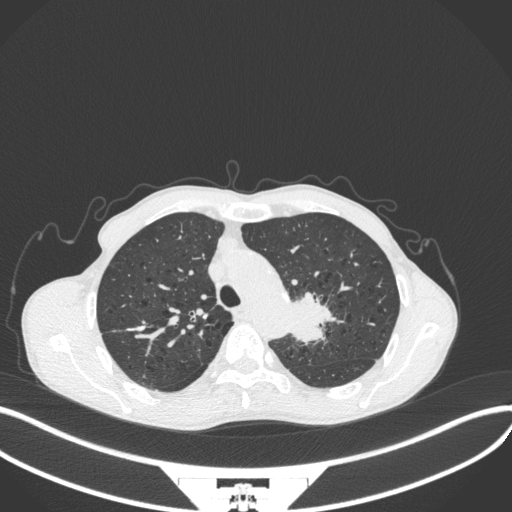
Chest CT, one axial slice; slice 314 of 394 in the series (ordered by position); reconstruction kernel B31f; 120 kVp; lung window (W 1500 / L -600 HU); 512 × 512 image matrix, field of view 400 × 400 mm. Male patient, age 65 years. Case-level facts recorded for this patient, not image findings: clinical TNM (as recorded): T2b N0 M0.
Outlined on this slice (rectangle marked by the reading radiologist):
- lung tumour (recorded histology: adenocarcinoma): box from (x=290, y=286) to (x=343, y=347) px